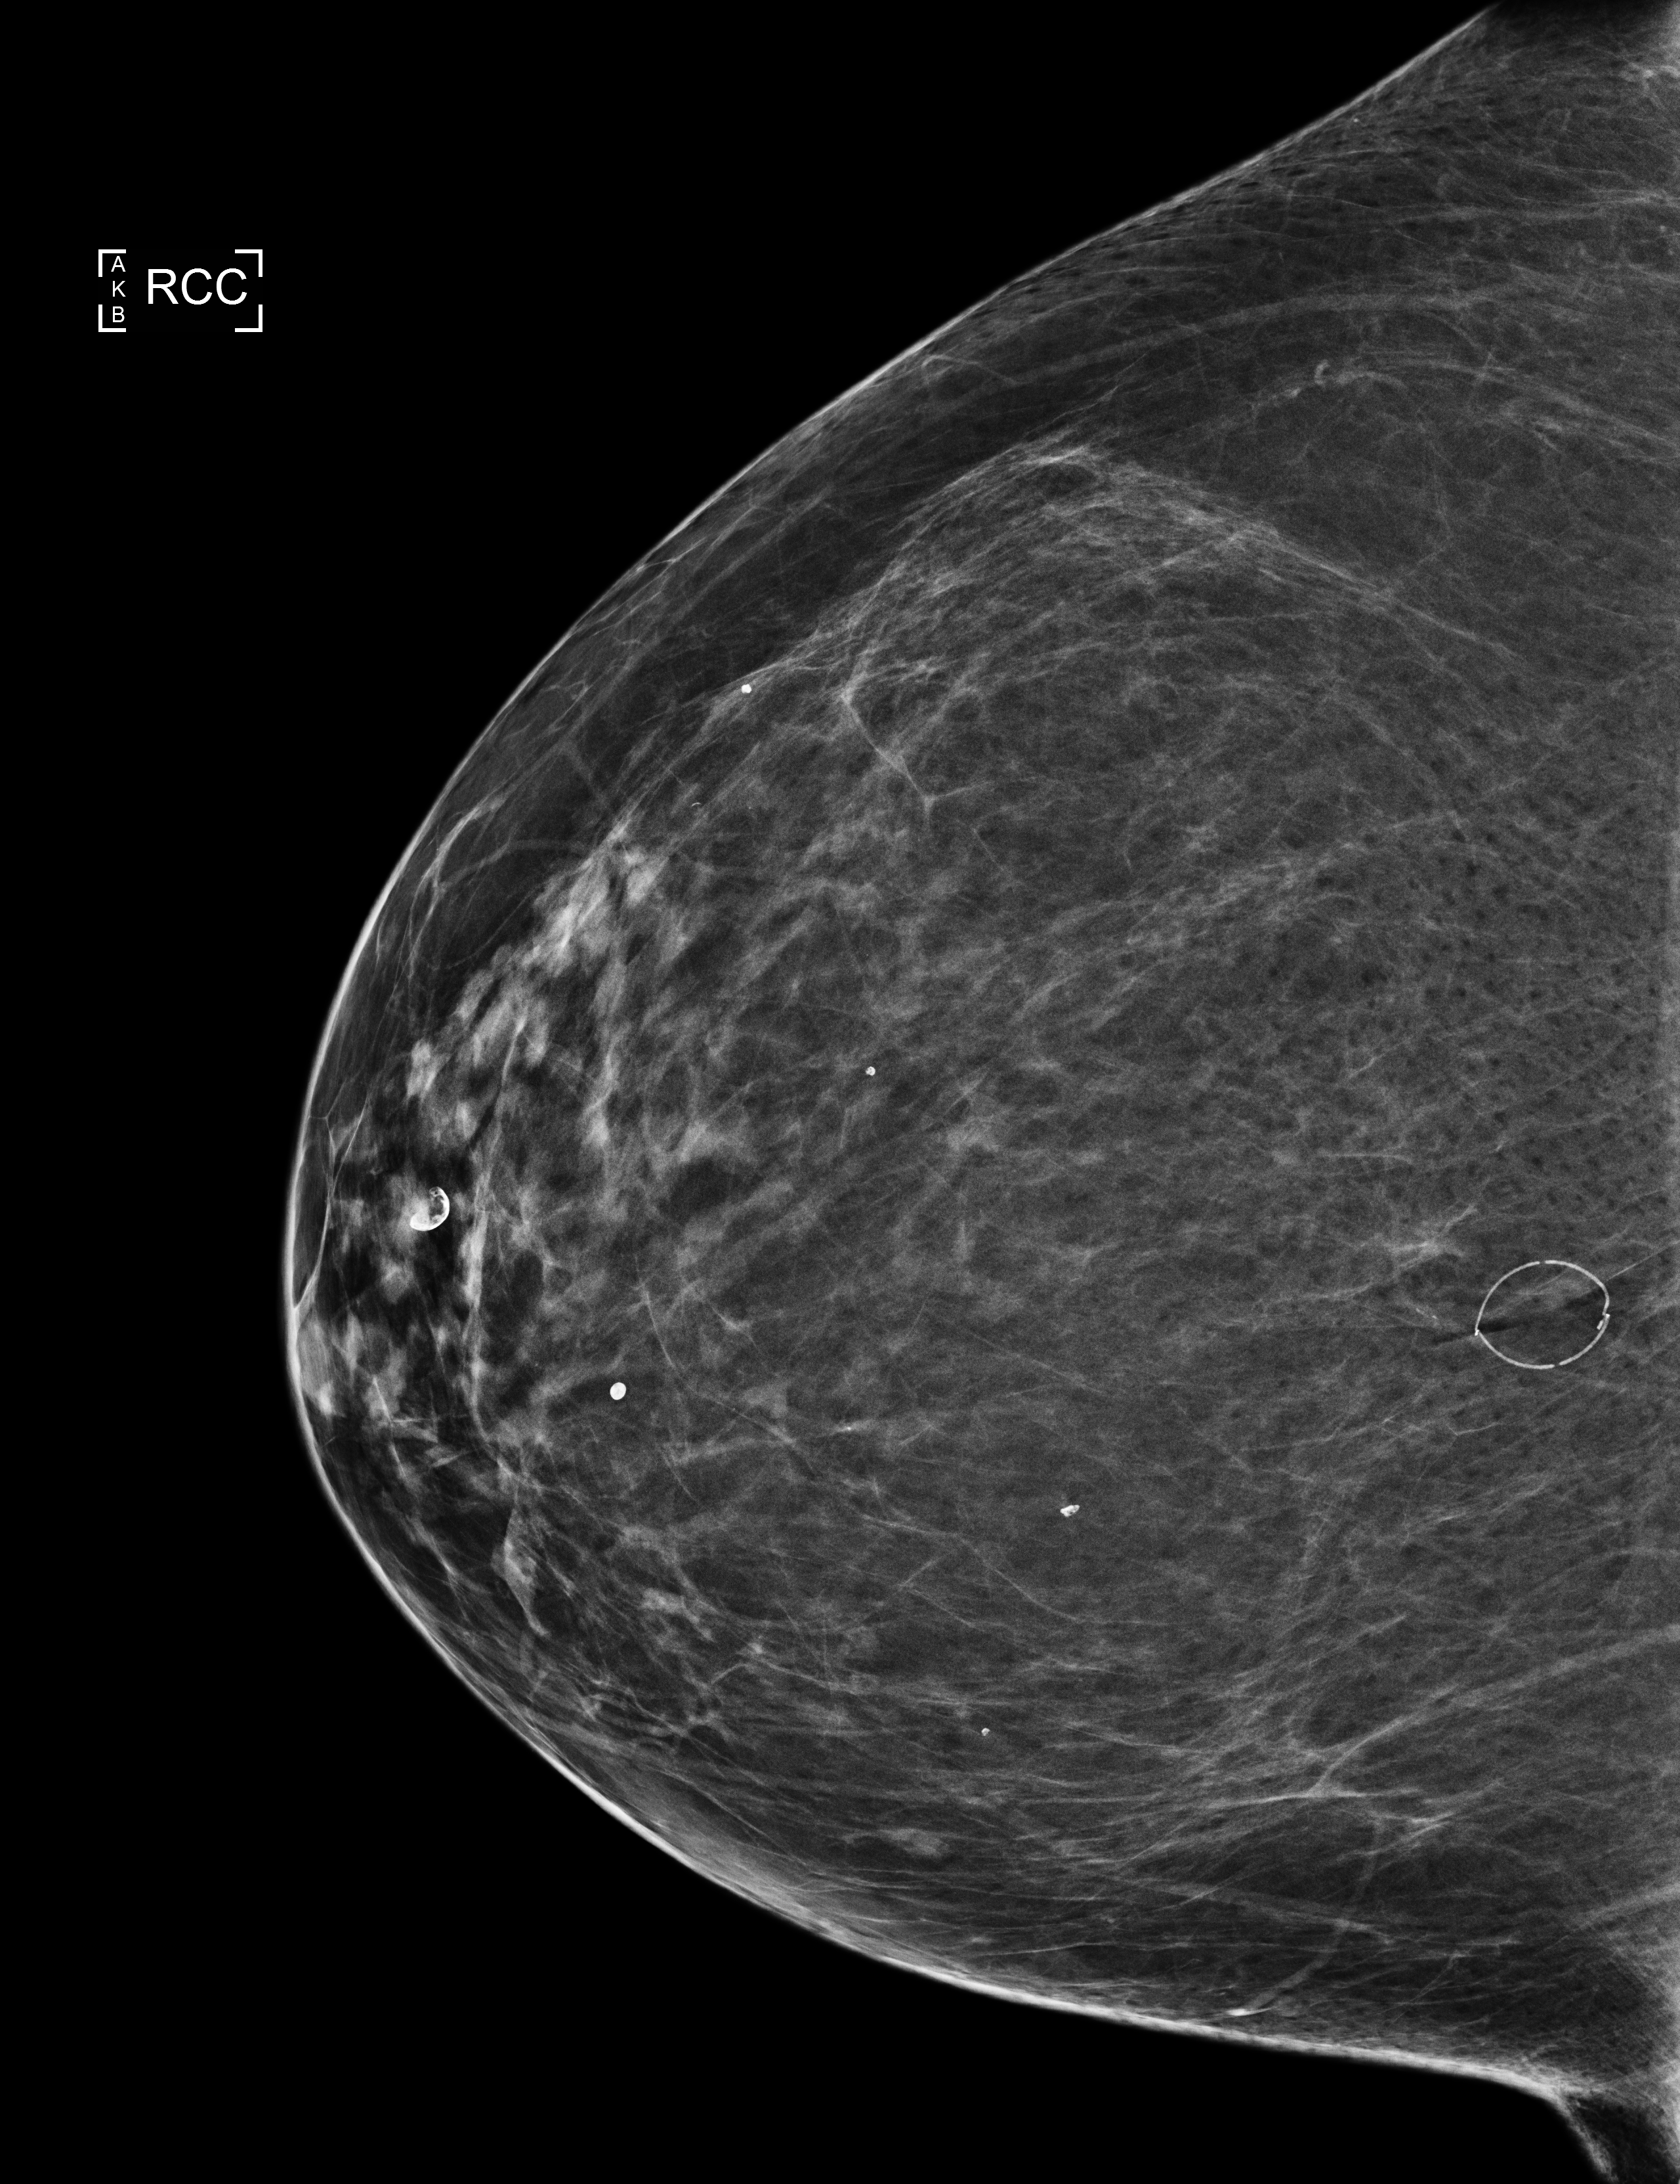
Digital mammogram (FFDM), right breast, craniocaudal (CC) view, screening examination, compressed breast thickness 63 mm. Patient: female, 66 years.
Breast density at the screening exam (both breasts): scattered fibroglandular densities (BI-RADS density category b). Final BI-RADS assessment for this screening round (tomosynthesis exam, both breasts): category 1. Recall: no recall after this screen.